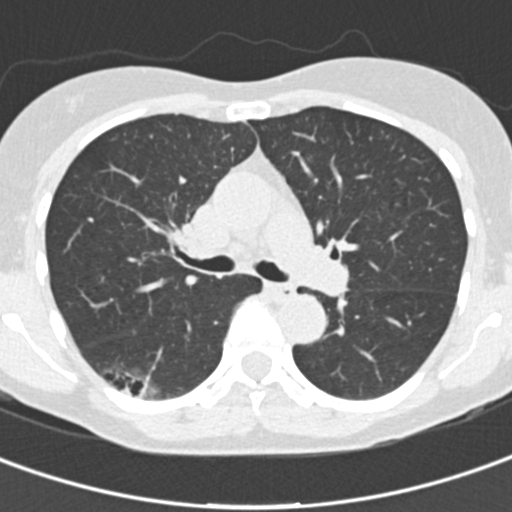
Low-dose screening chest CT, axial slice; baseline annual screen; lung window (W 1500 / L -600 HU). Female participant, aged 64 years at enrolment. Current smoker at enrolment.
Expert reader's lesion annotation, bounding box <83,348,175,415> (left, top, right, bottom; pixels). Screening reader's record for this exam (one nodule recorded; not confirmed to be the boxed lesion): non-calcified nodule or mass ≥4 mm, right lower lobe, 31 × 15 mm, poorly defined margins, ground glass attenuation.